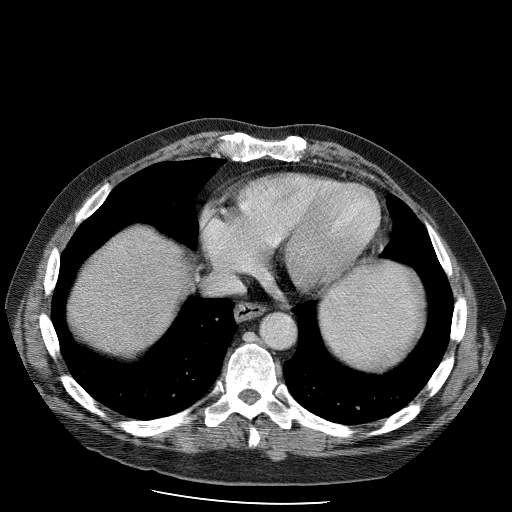
Contrast-enhanced abdominal CT (liver protocol), one axial slice. Slice 94 of 98 in the series (ordered by position). Reconstruction kernel STANDARD. Soft-tissue window (W 400 / L 40 HU). 2.5 mm slice thickness. 512 × 512 image matrix. Case-level facts recorded for this patient, not image findings: diagnosis: hepatocellular carcinoma (patient treated with transarterial chemoembolisation; whether this scan precedes or follows treatment is not stated here); TNM stage (as recorded): Stage-II; Child-Pugh class: B; tumour differentiation: moderately differentiated; tumour nodularity: uninodular.
Structures marked on this image (semi-automatic segmentation, software-assisted and operator-edited):
- liver parenchyma outside the tumour (the mass and vessels are separate outlines, so this box may not span the whole liver): bounding box <70,232,182,346> (left, top, right, bottom; pixels)